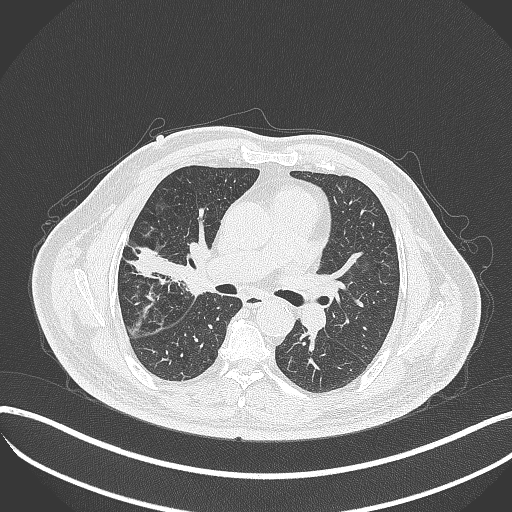
Chest CT, one axial slice; slice 207 of 401 in the series (ordered by position); reconstruction kernel B70f; 120 kVp; lung window (W 1500 / L -600 HU); 1 mm slice thickness; 512 × 512 image matrix, field of view 400 × 400 mm. Male patient, age 72 years. From the clinical record (not read from this slice): clinical TNM (as recorded): T1c N0 M0.
Outlined on this slice (rectangle marked by the reading radiologist):
- lung tumour (recorded histology: squamous cell carcinoma): box from (x=175, y=239) to (x=213, y=303) px